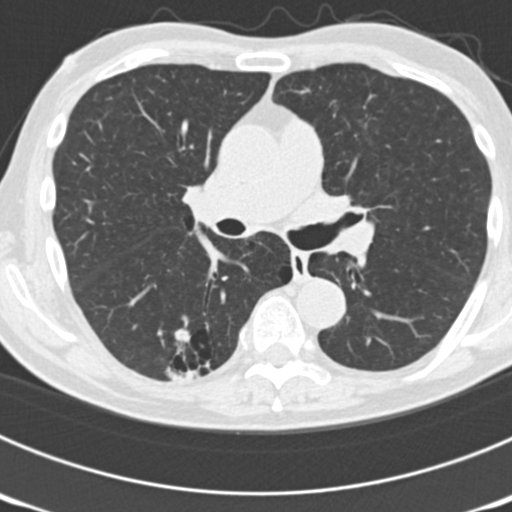
Low-dose screening chest CT, one axial slice; position 108 of 177 along the scan axis; reconstruction kernel B30f; 120 kVp; lung window (W 1500 / L -600 HU); 2 mm slice thickness; 512 × 512 image matrix, field of view 300 × 300 mm.
Outlined on this slice (expert manual segmentation):
- lesion 5 (nodule, lower lobe of right lung): bounding box <168,365,196,382> (left, top, right, bottom; pixels)
- lesion 7 (nodule, lower lobe of right lung): <173,328,193,346>